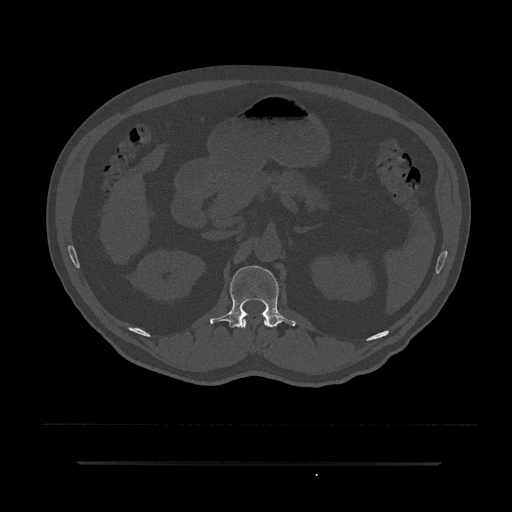
CT including the spine, one axial slice. Slice 158 of 797 in the series (ordered by position). Reconstruction kernel Br40s/3. 120 kVp. Bone window (W 1800 / L 400 HU). 512 × 512 image matrix, field of view 464 × 464 mm. Male patient, age 59 years. Case-level facts recorded for this patient, not image findings: primary cancer: bile ducts.
Annotated regions visible in this slice (semi-automatic segmentation, software-assisted and operator-edited):
- L1 vertebra: bounding box [x1, y1, x2, y2] px = [210, 265, 296, 328]
- T12 vertebra: [241, 319, 268, 329]